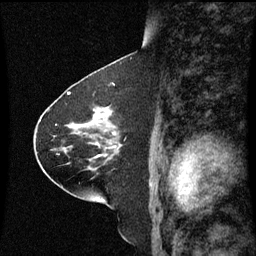
Breast MRI (dynamic contrast-enhanced), one sagittal slice; slice 36 of 60 in the series (ordered by position); dynamic contrast-enhanced series, image 2 of 3 at this slice position (ordered by acquisition); 1.5 T; TE 4.2 ms, TR 8.9 ms; 2 mm slice thickness; 256 × 256 image matrix, field of view 200 × 200 mm. Patient: female, 63 years. From the clinical record (not read from this slice): setting: breast cancer imaged before/during neoadjuvant chemotherapy; receptor status: HR-positive, HER2-negative.
Outlined on this slice (semi-automatic segmentation, software-assisted and operator-edited):
- analysis volume of interest (the breast-tissue region the enhancement analysis was run in; not a lesion): bounding box <77,106,123,151> (left, top, right, bottom; pixels)
- tumour enhancement mask (voxels above the 70 % enhancement threshold inside the analysis volume of interest): <94,112,115,135>